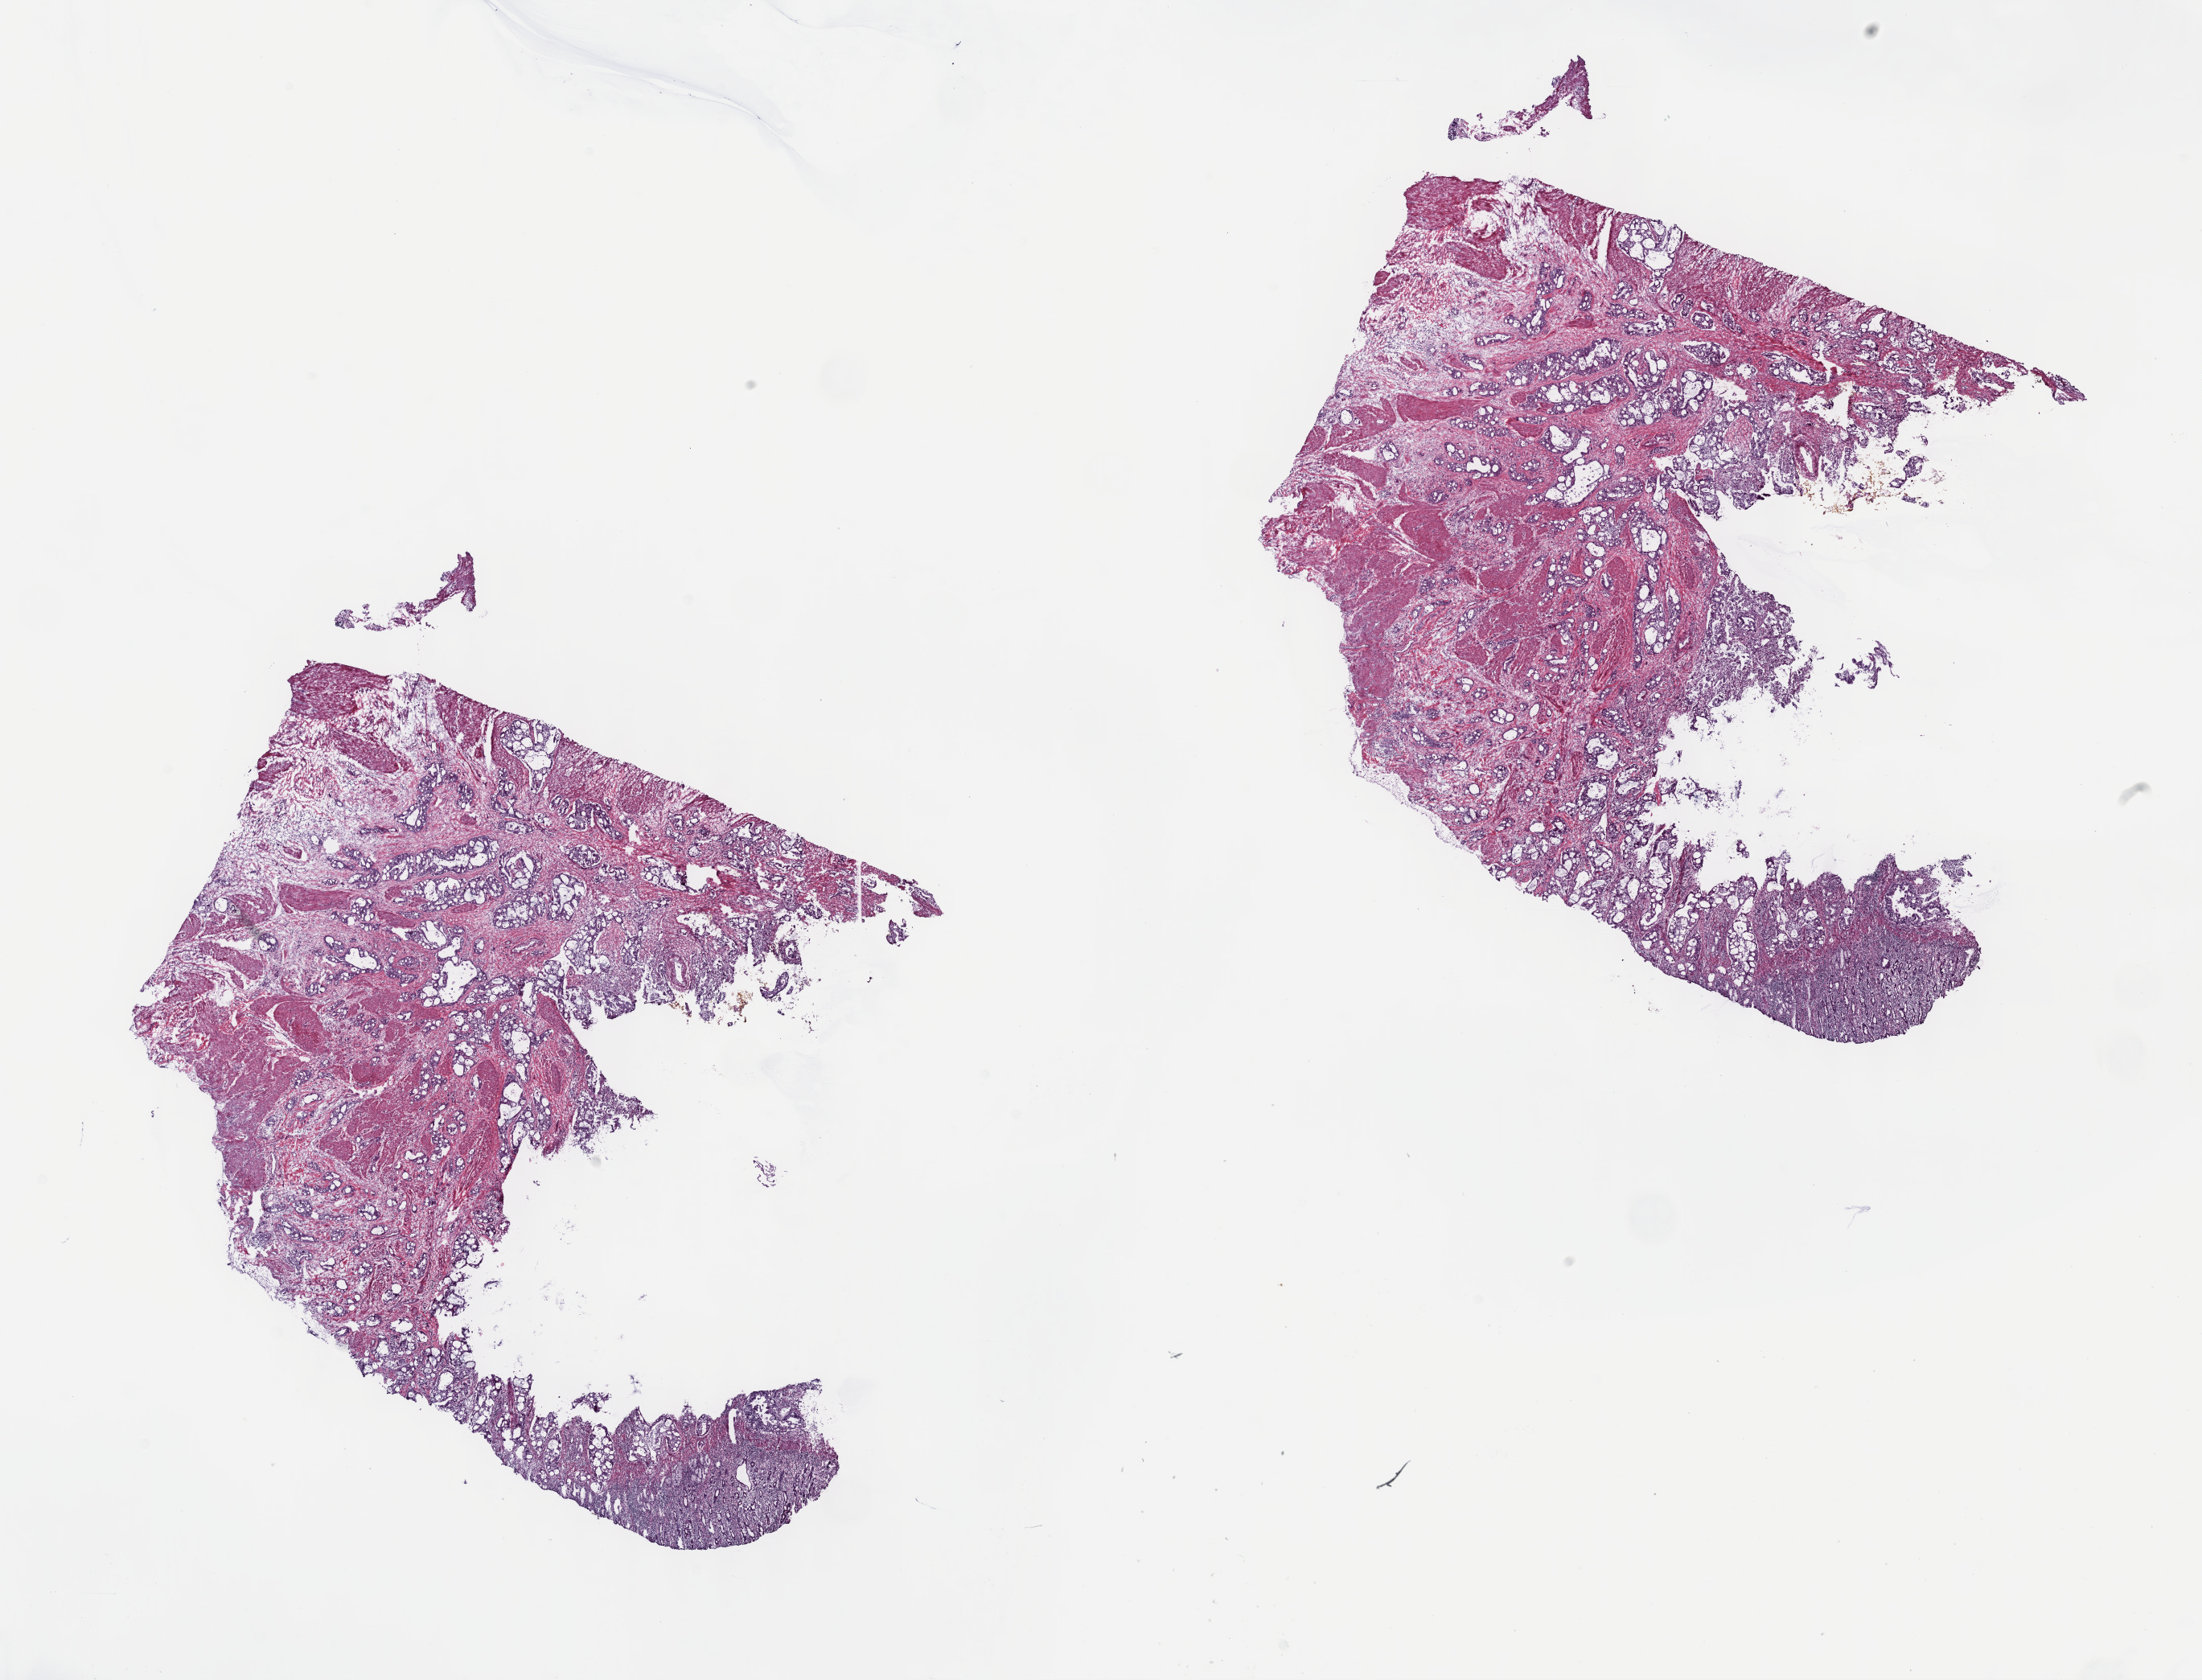
Whole-slide histology image, Hematoxylin and eosin (H&E) stained — whole scanned area (about 22.1 x 16.9 mm, slide scanned at 40x) shown as a low-resolution overview. Frozen section from the top of the tissue portion. Primary tumour sample from the pancreas. Male patient; age at initial diagnosis 71 years.
Pathologic diagnosis: Infiltrating duct carcinoma, NOS (head of pancreas).